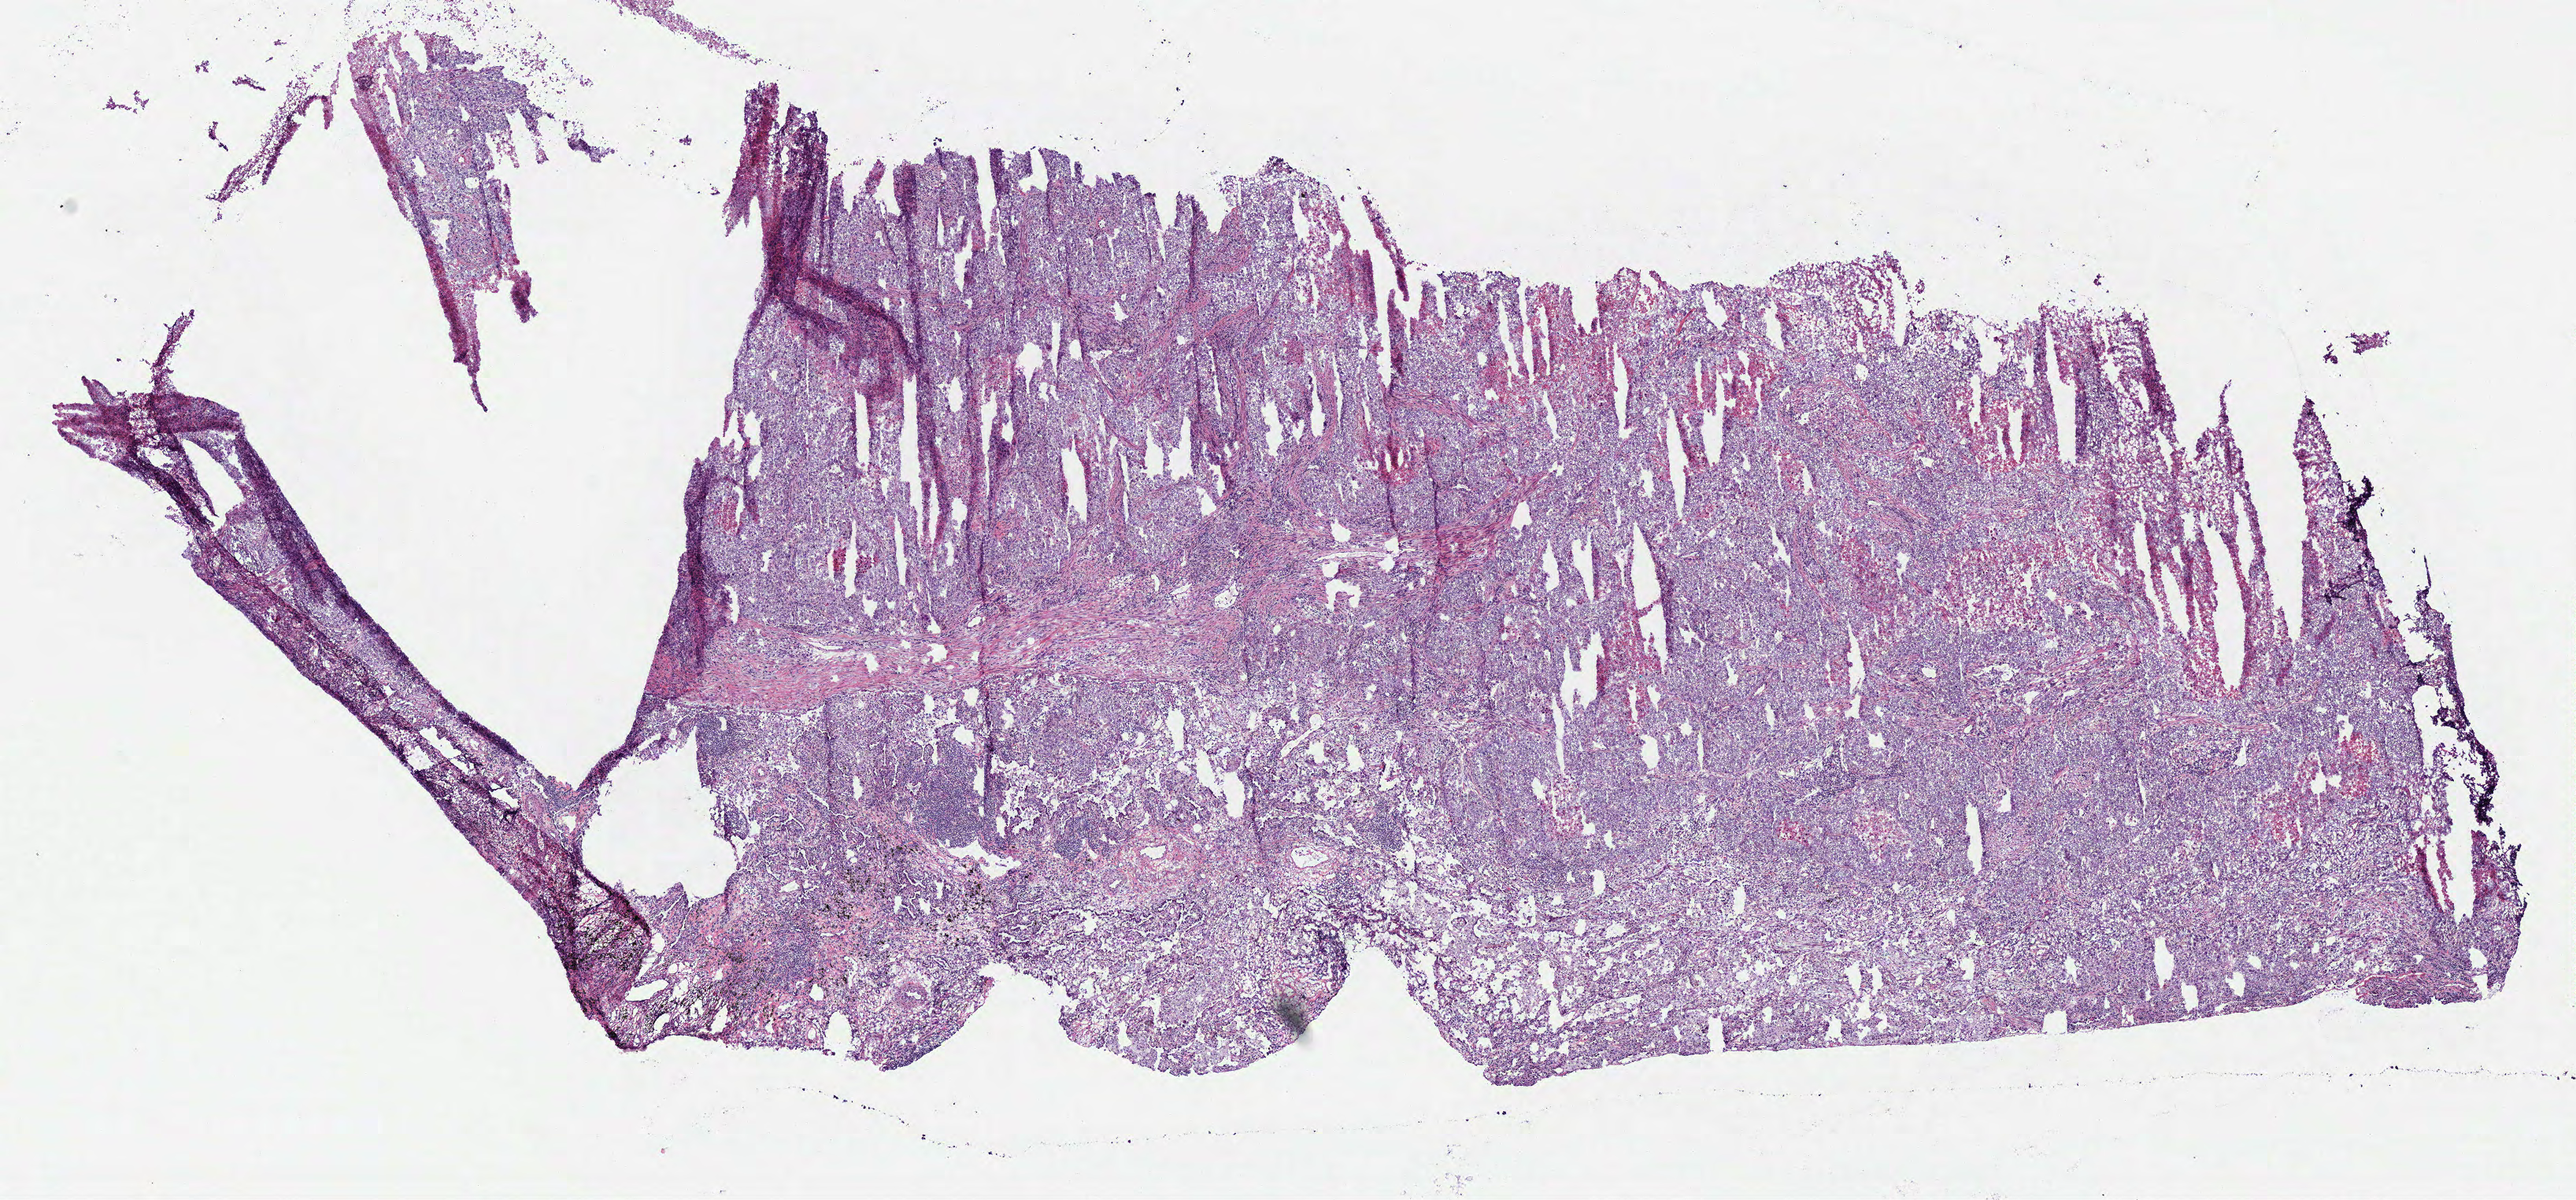
Hematoxylin and eosin (H&E) stained whole-slide image — low-resolution overview of the scanned area, about 12.9 x 6.0 mm (acquisition: 40x scan); frozen section; sample: primary tumour, lung. Patient: female, age at initial diagnosis 81 years. Pathologist review of this section (percent, as recorded): tumour cells 67%, tumour nuclei 70%, normal cells 15%, stromal cells 10%, necrosis 8%.
* diagnosis: Clear cell adenocarcinoma, NOS (upper lobe, lung)
* TNM: T1 N2 MX
* AJCC pathologic stage: IIIA